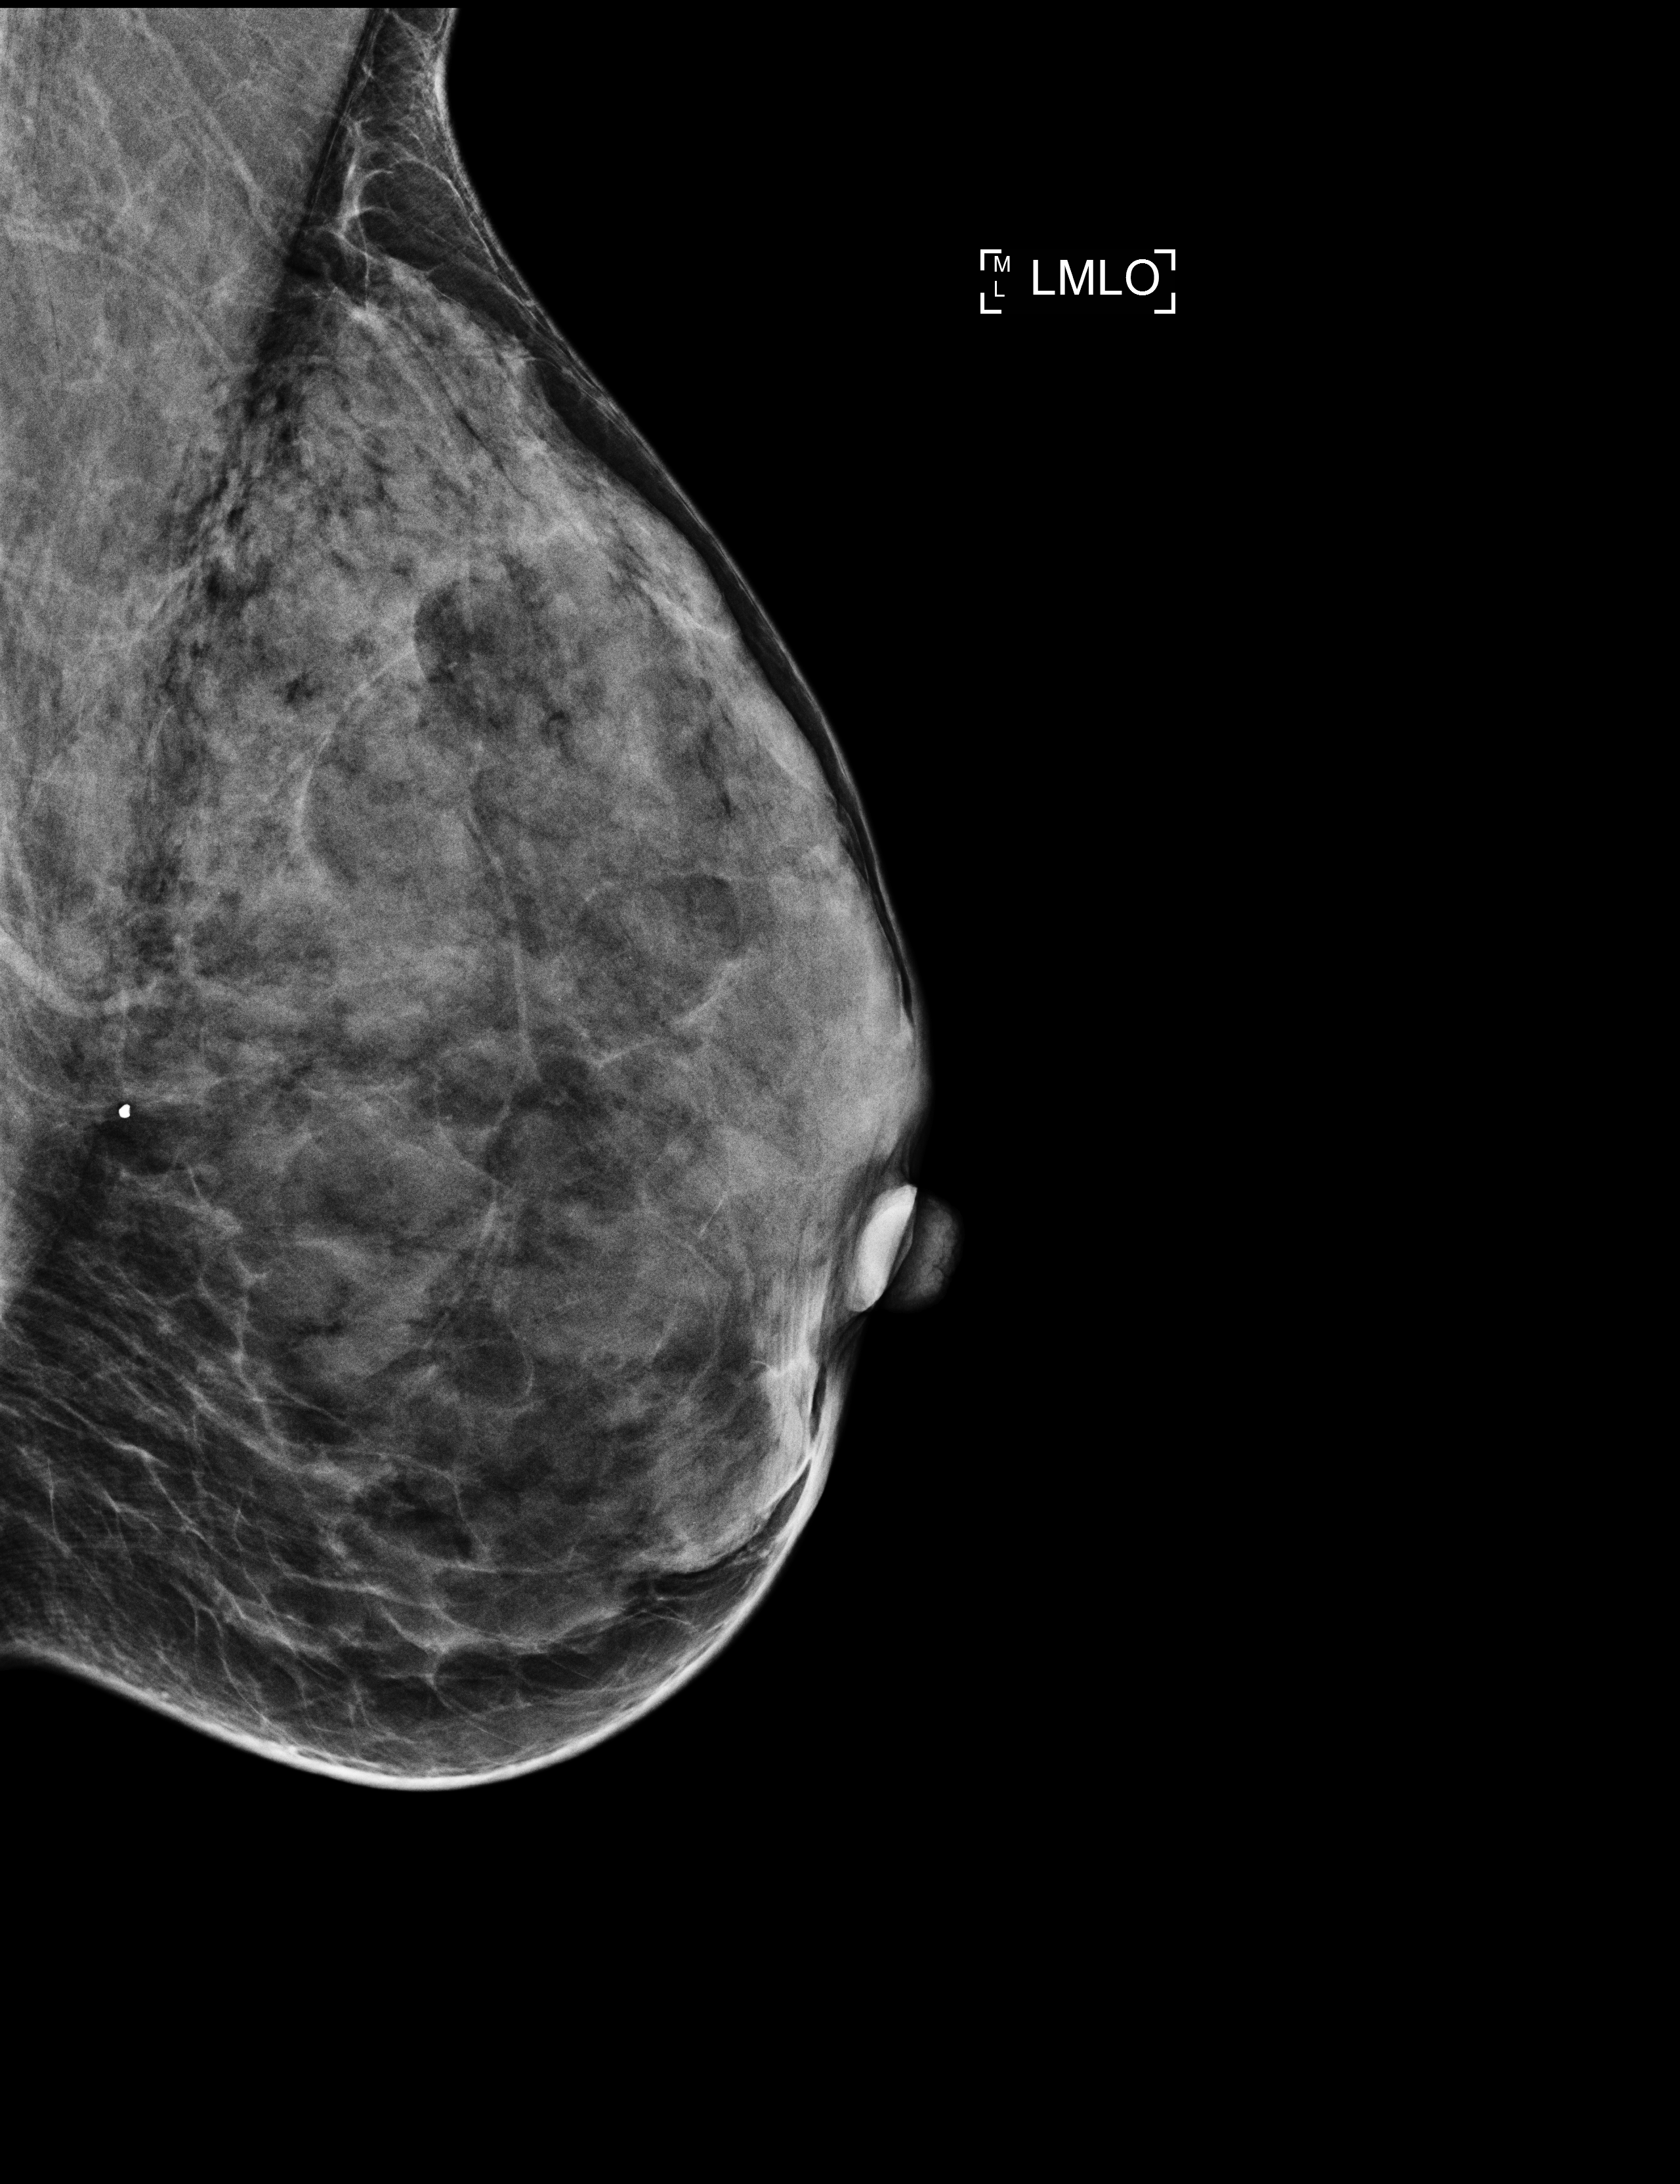
Screening examination, system: Selenia Dimensions. Female patient, age 56 years.
Image type: full-field digital mammogram. Breast: left. Projection: medio-lateral oblique projection.